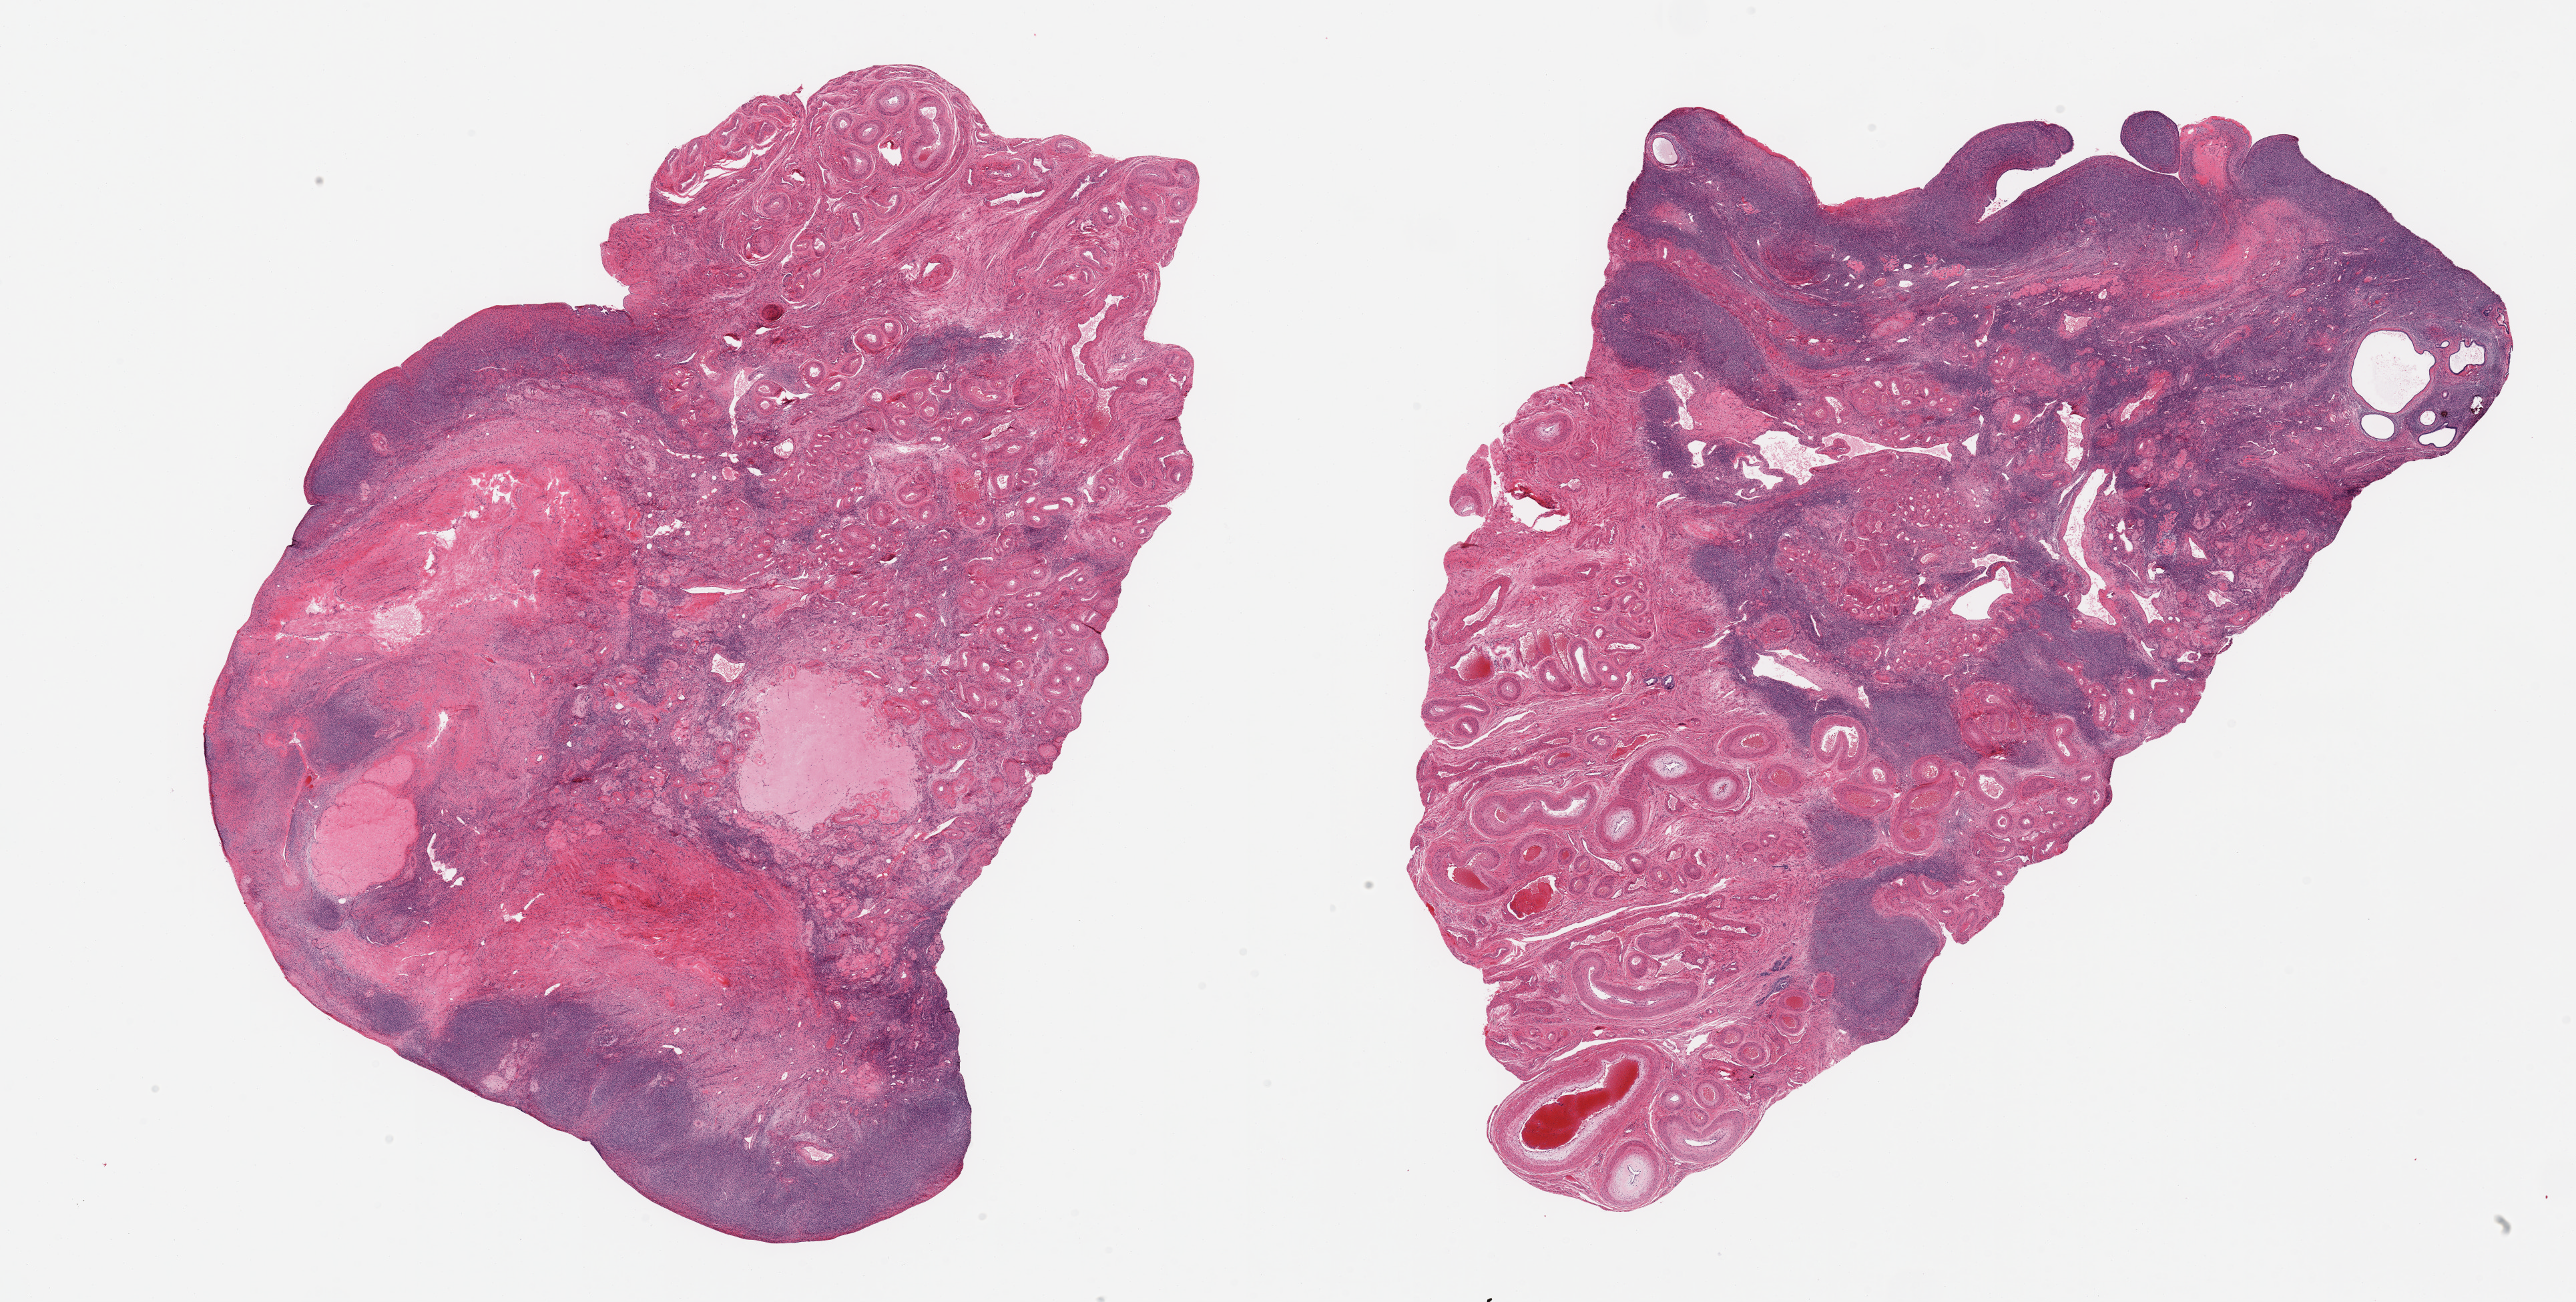
Haematoxylin and eosin whole-slide image, low-resolution overview of the scanned area, about 30.5 x 15.4 mm. PAXgene-fixed paraffin-embedded (PFPE) section. Target tissue: ovary. Donor tissue sample. Donor: female.
• review note (as recorded): 2 pieces; few surface epithelial inclusion glands and adjacent psammoma bodies; significant portion of both is hilum/vessels